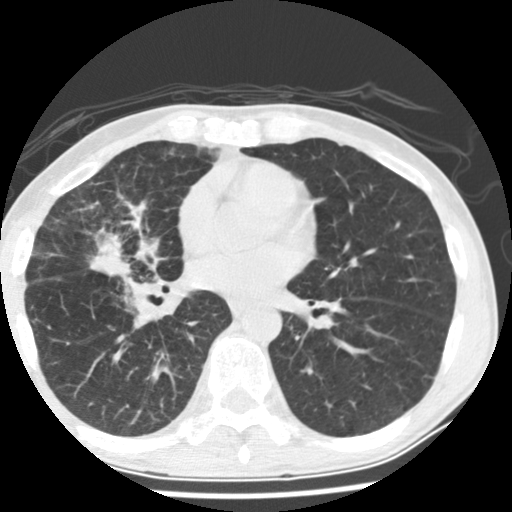
Low-dose screening chest CT, one axial slice; slice 76 of 162 in the series (ordered by position); reconstruction kernel STANDARD; 120 kVp; lung window (W 1500 / L -600 HU); 2.5 mm slice thickness; 512 × 512 image matrix, field of view 310 × 310 mm.
Annotated regions visible in this slice (outlined manually by an expert reader):
- lesion 1 (tumor, middle lobe of right lung): bounding box <74,235,116,277> (left, top, right, bottom; pixels)